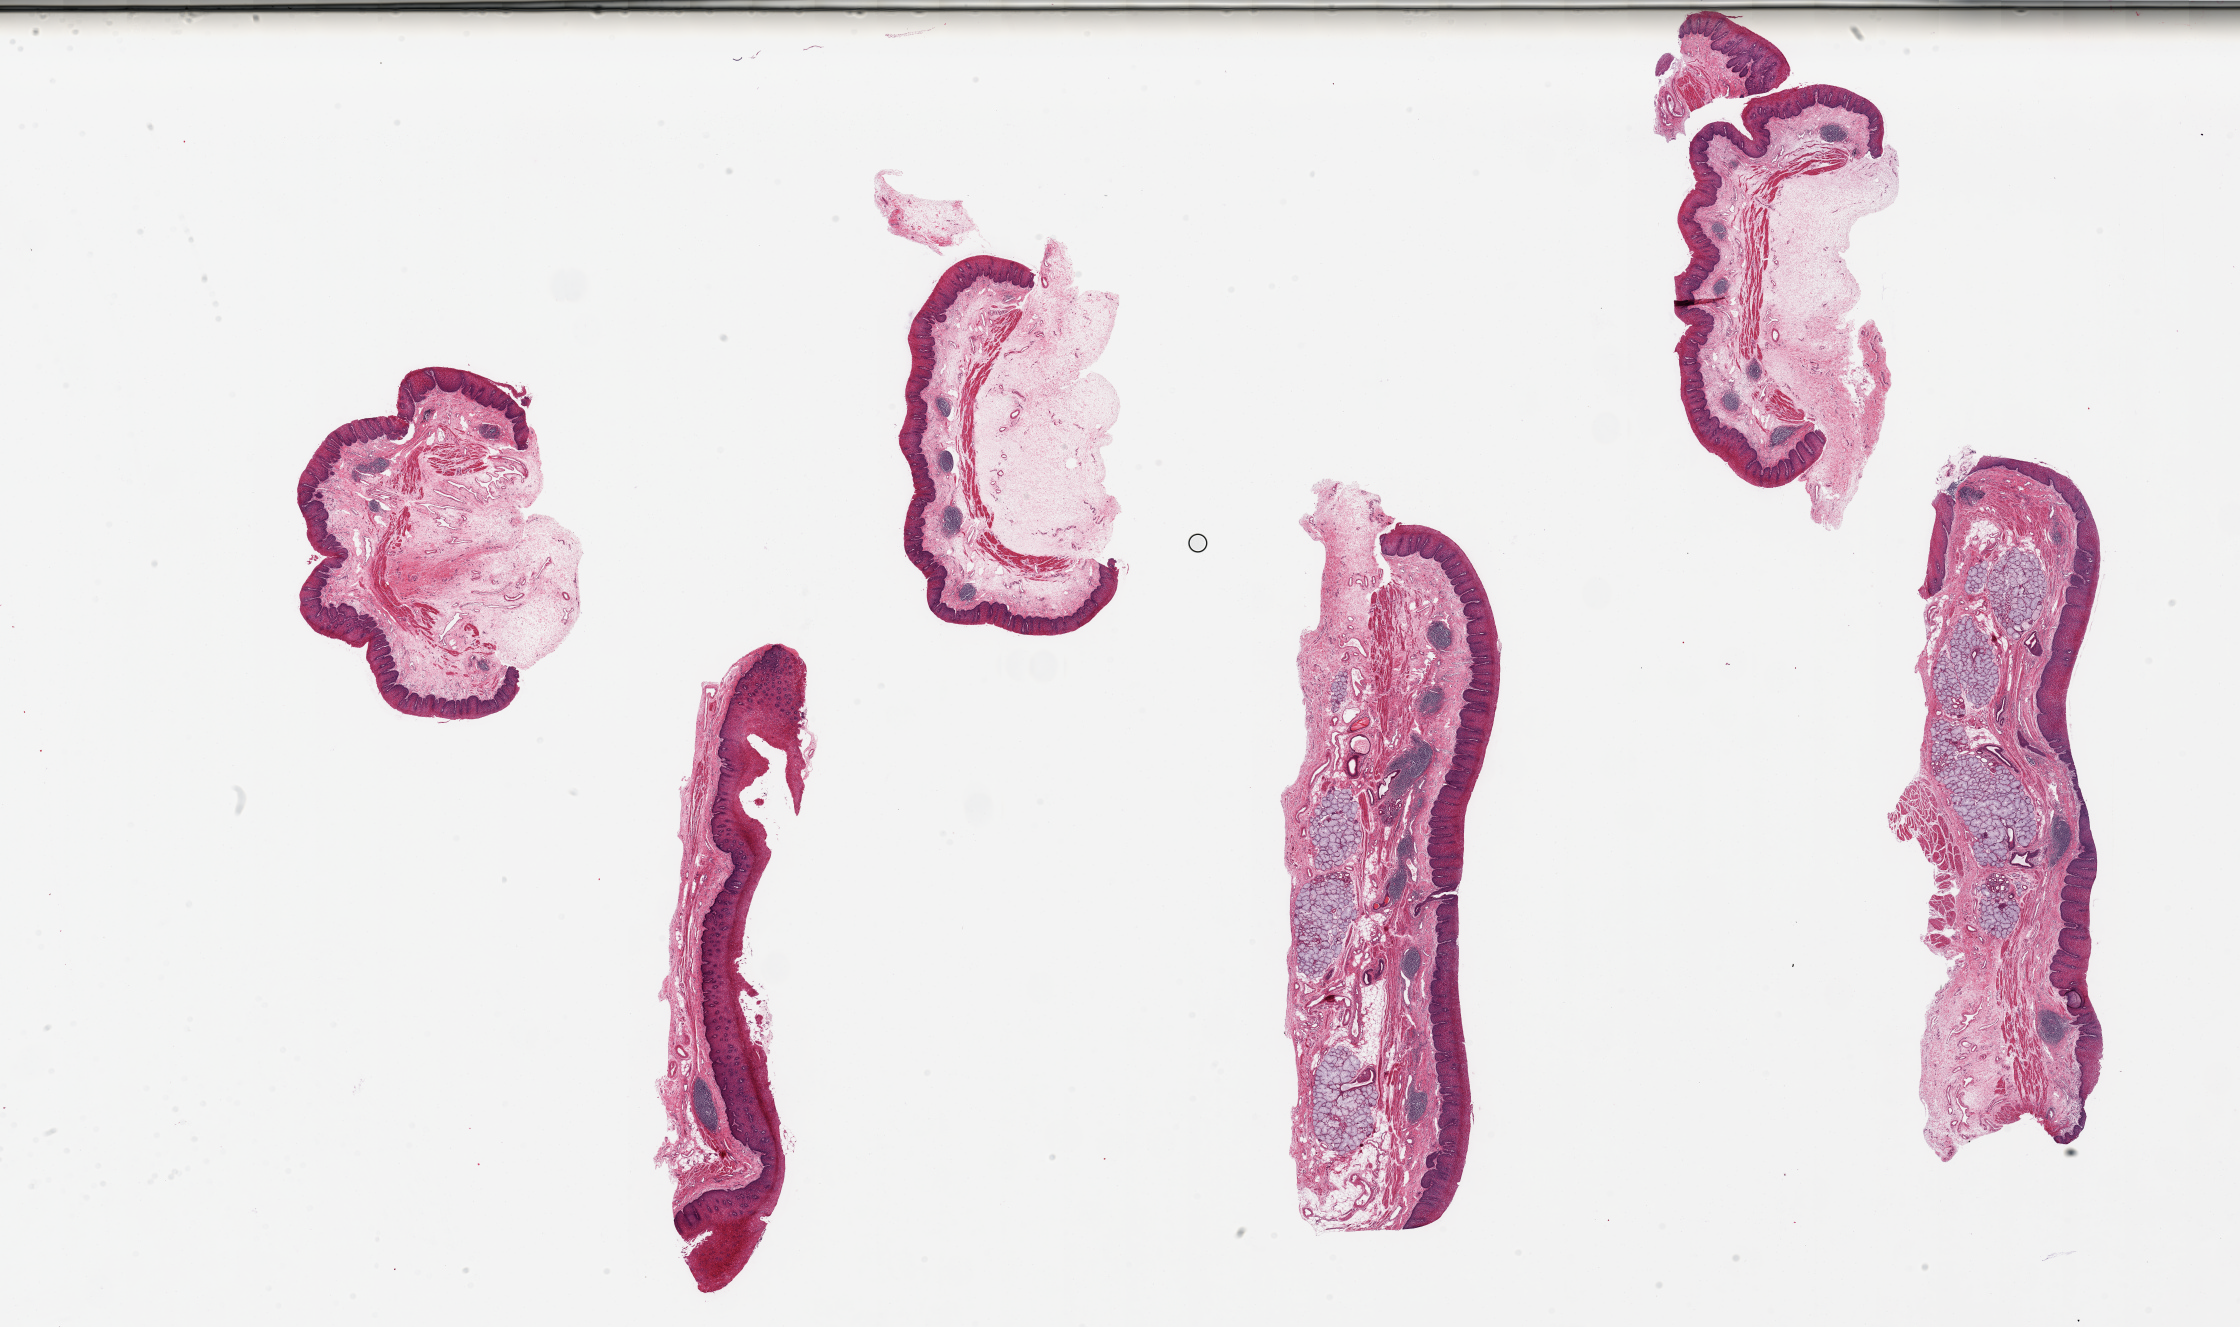
Digitized haematoxylin and eosin-stained section, brightfield, shown as a low-resolution overview of the whole scanned area (about 35.4 x 21.0 mm), PAXgene-fixed paraffin-embedded (PFPE) section, target tissue: esophageal mucous membrane, tissue donor sample. Donor sex: male.
Reviewer comment on this tissue sample: 6 pieces, up to 12x3mm; Chronic inflammation and squamous hyperplasia. Abundant submucosal glands in the 2 largest pieces.